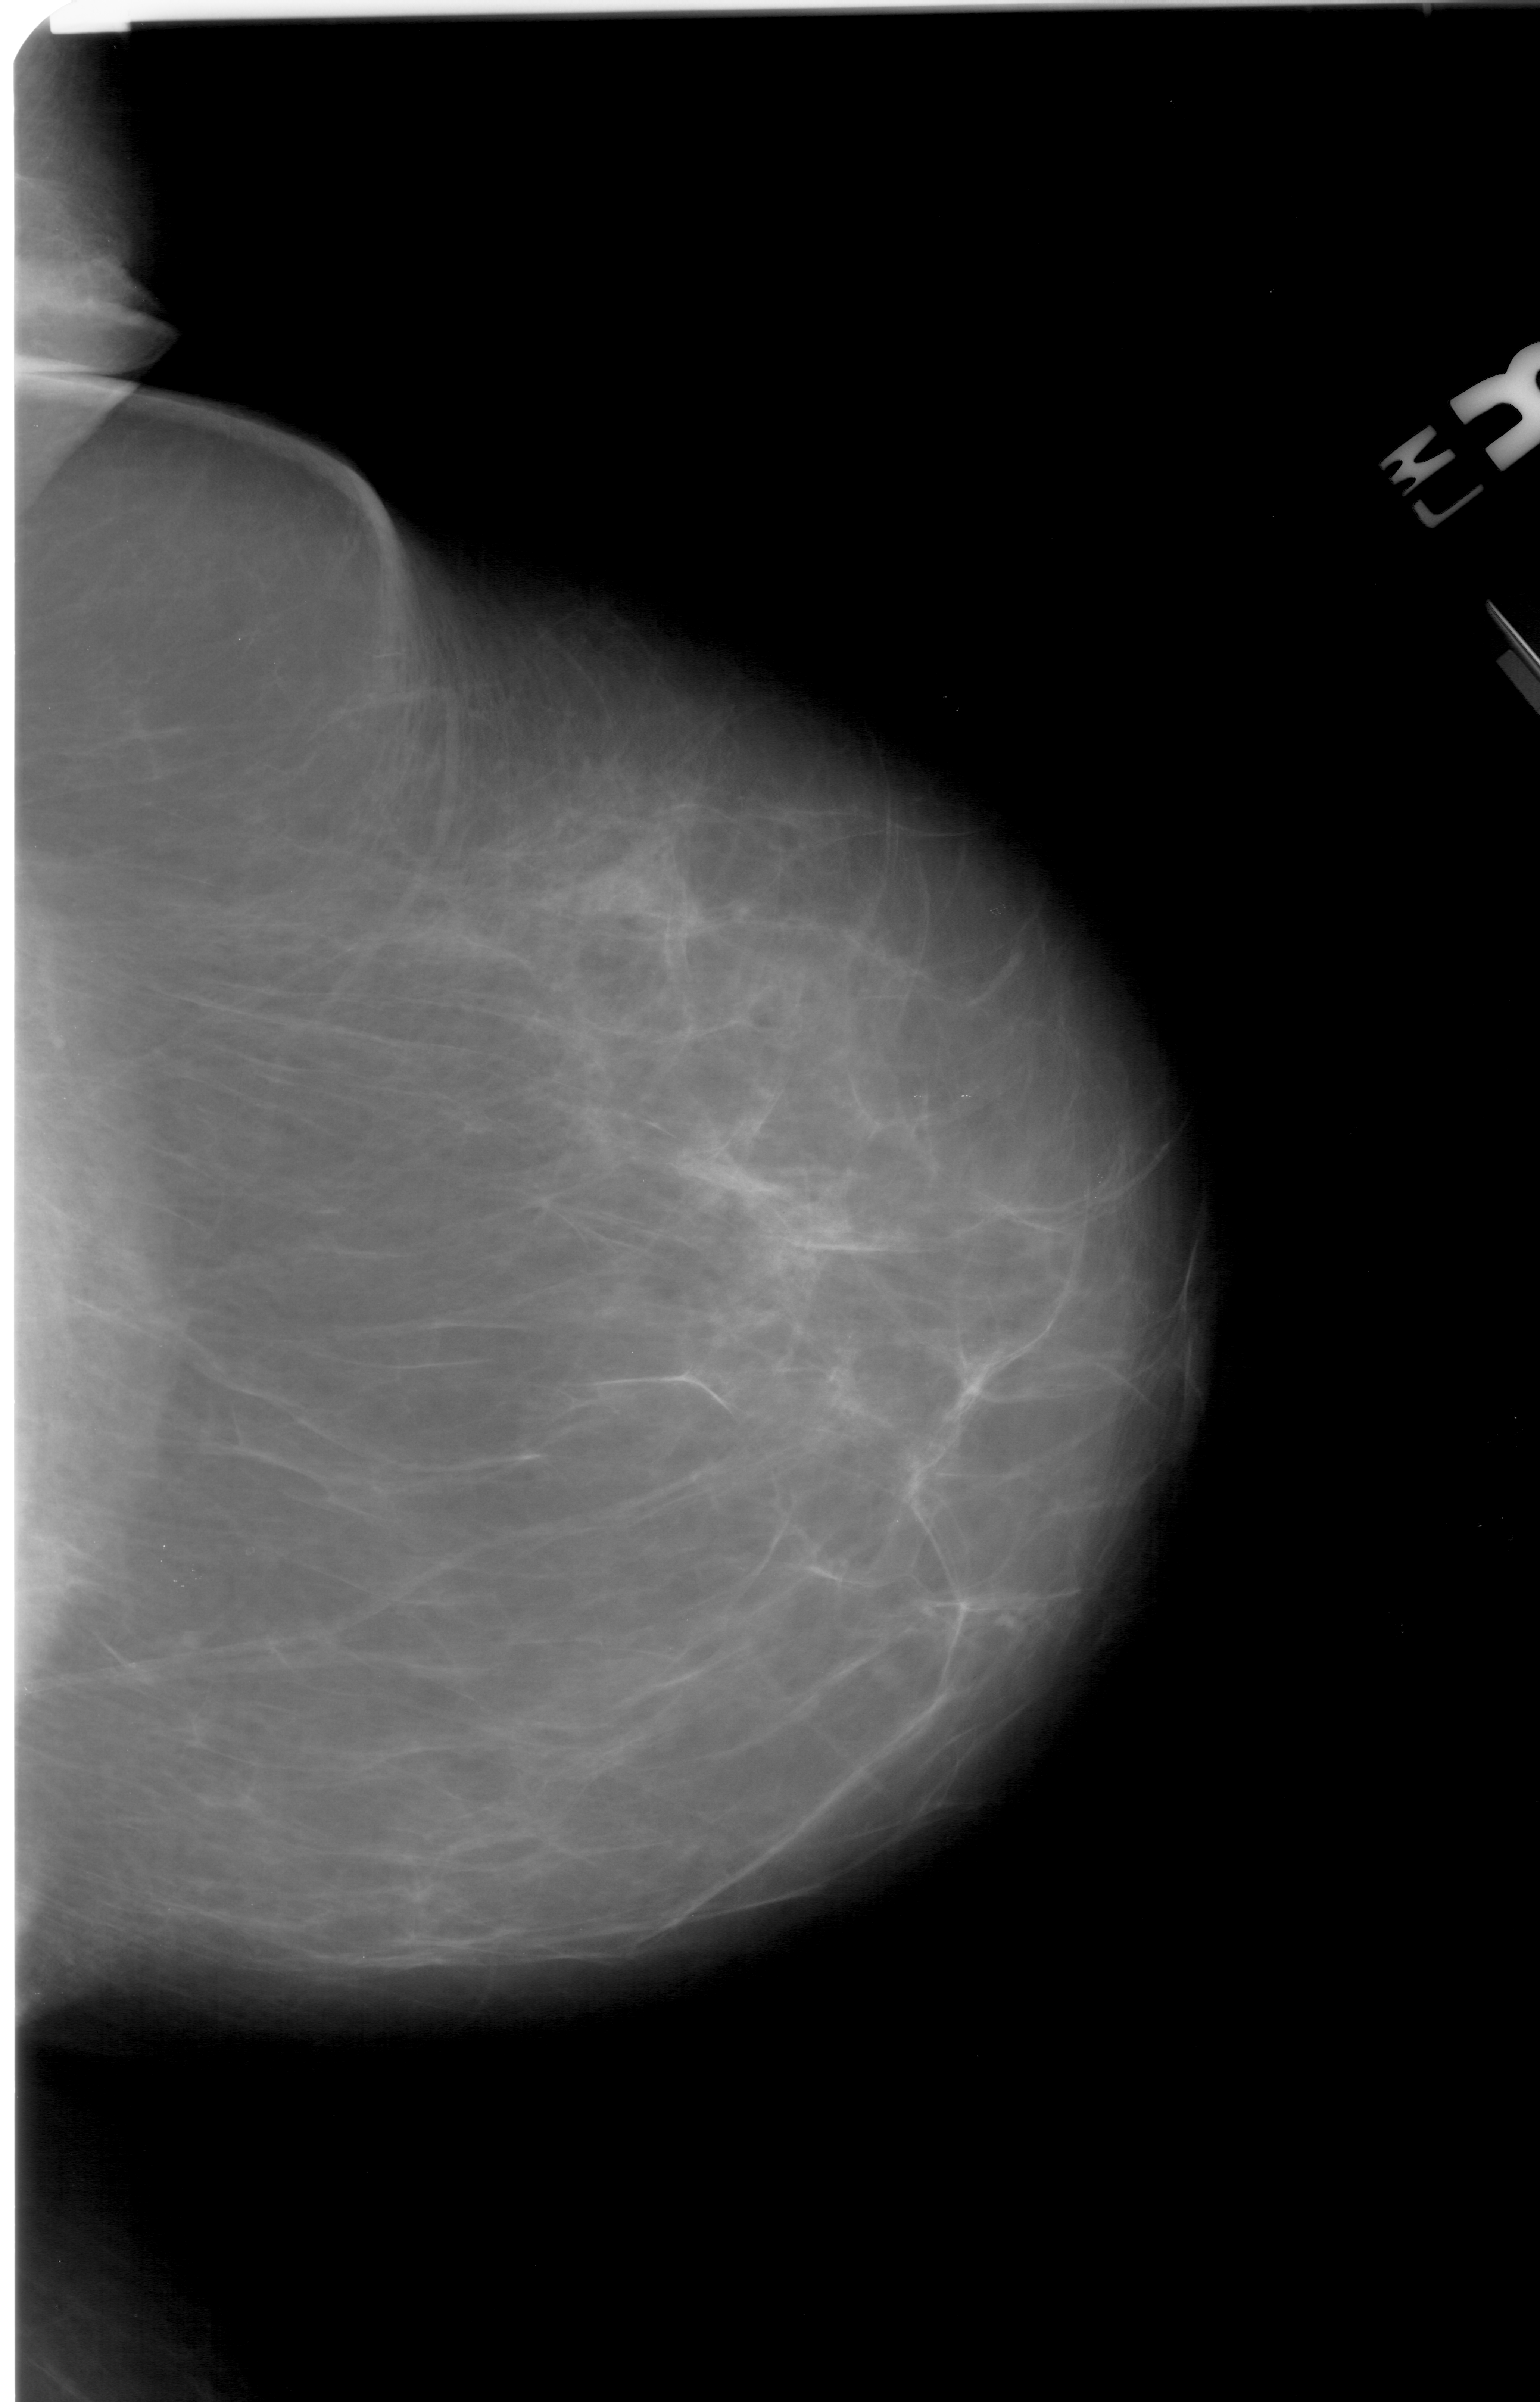
Digitized screen-film mammogram; right breast; craniocaudal (CC) view; breast composition: scattered fibroglandular densities (BI-RADS density category 2 of 4); 1540 × 2402 image matrix.
Expert-marked regions of interest on this image (one box per marked abnormality):
- mass, shape oval, margins obscured; BI-RADS assessment category 4; subtlety rating 3 on a 1 (subtle) to 5 (obvious) scale; pathology result (as recorded, not read from the image): benign: bounding box <575,842,679,935> (left, top, right, bottom; pixels)